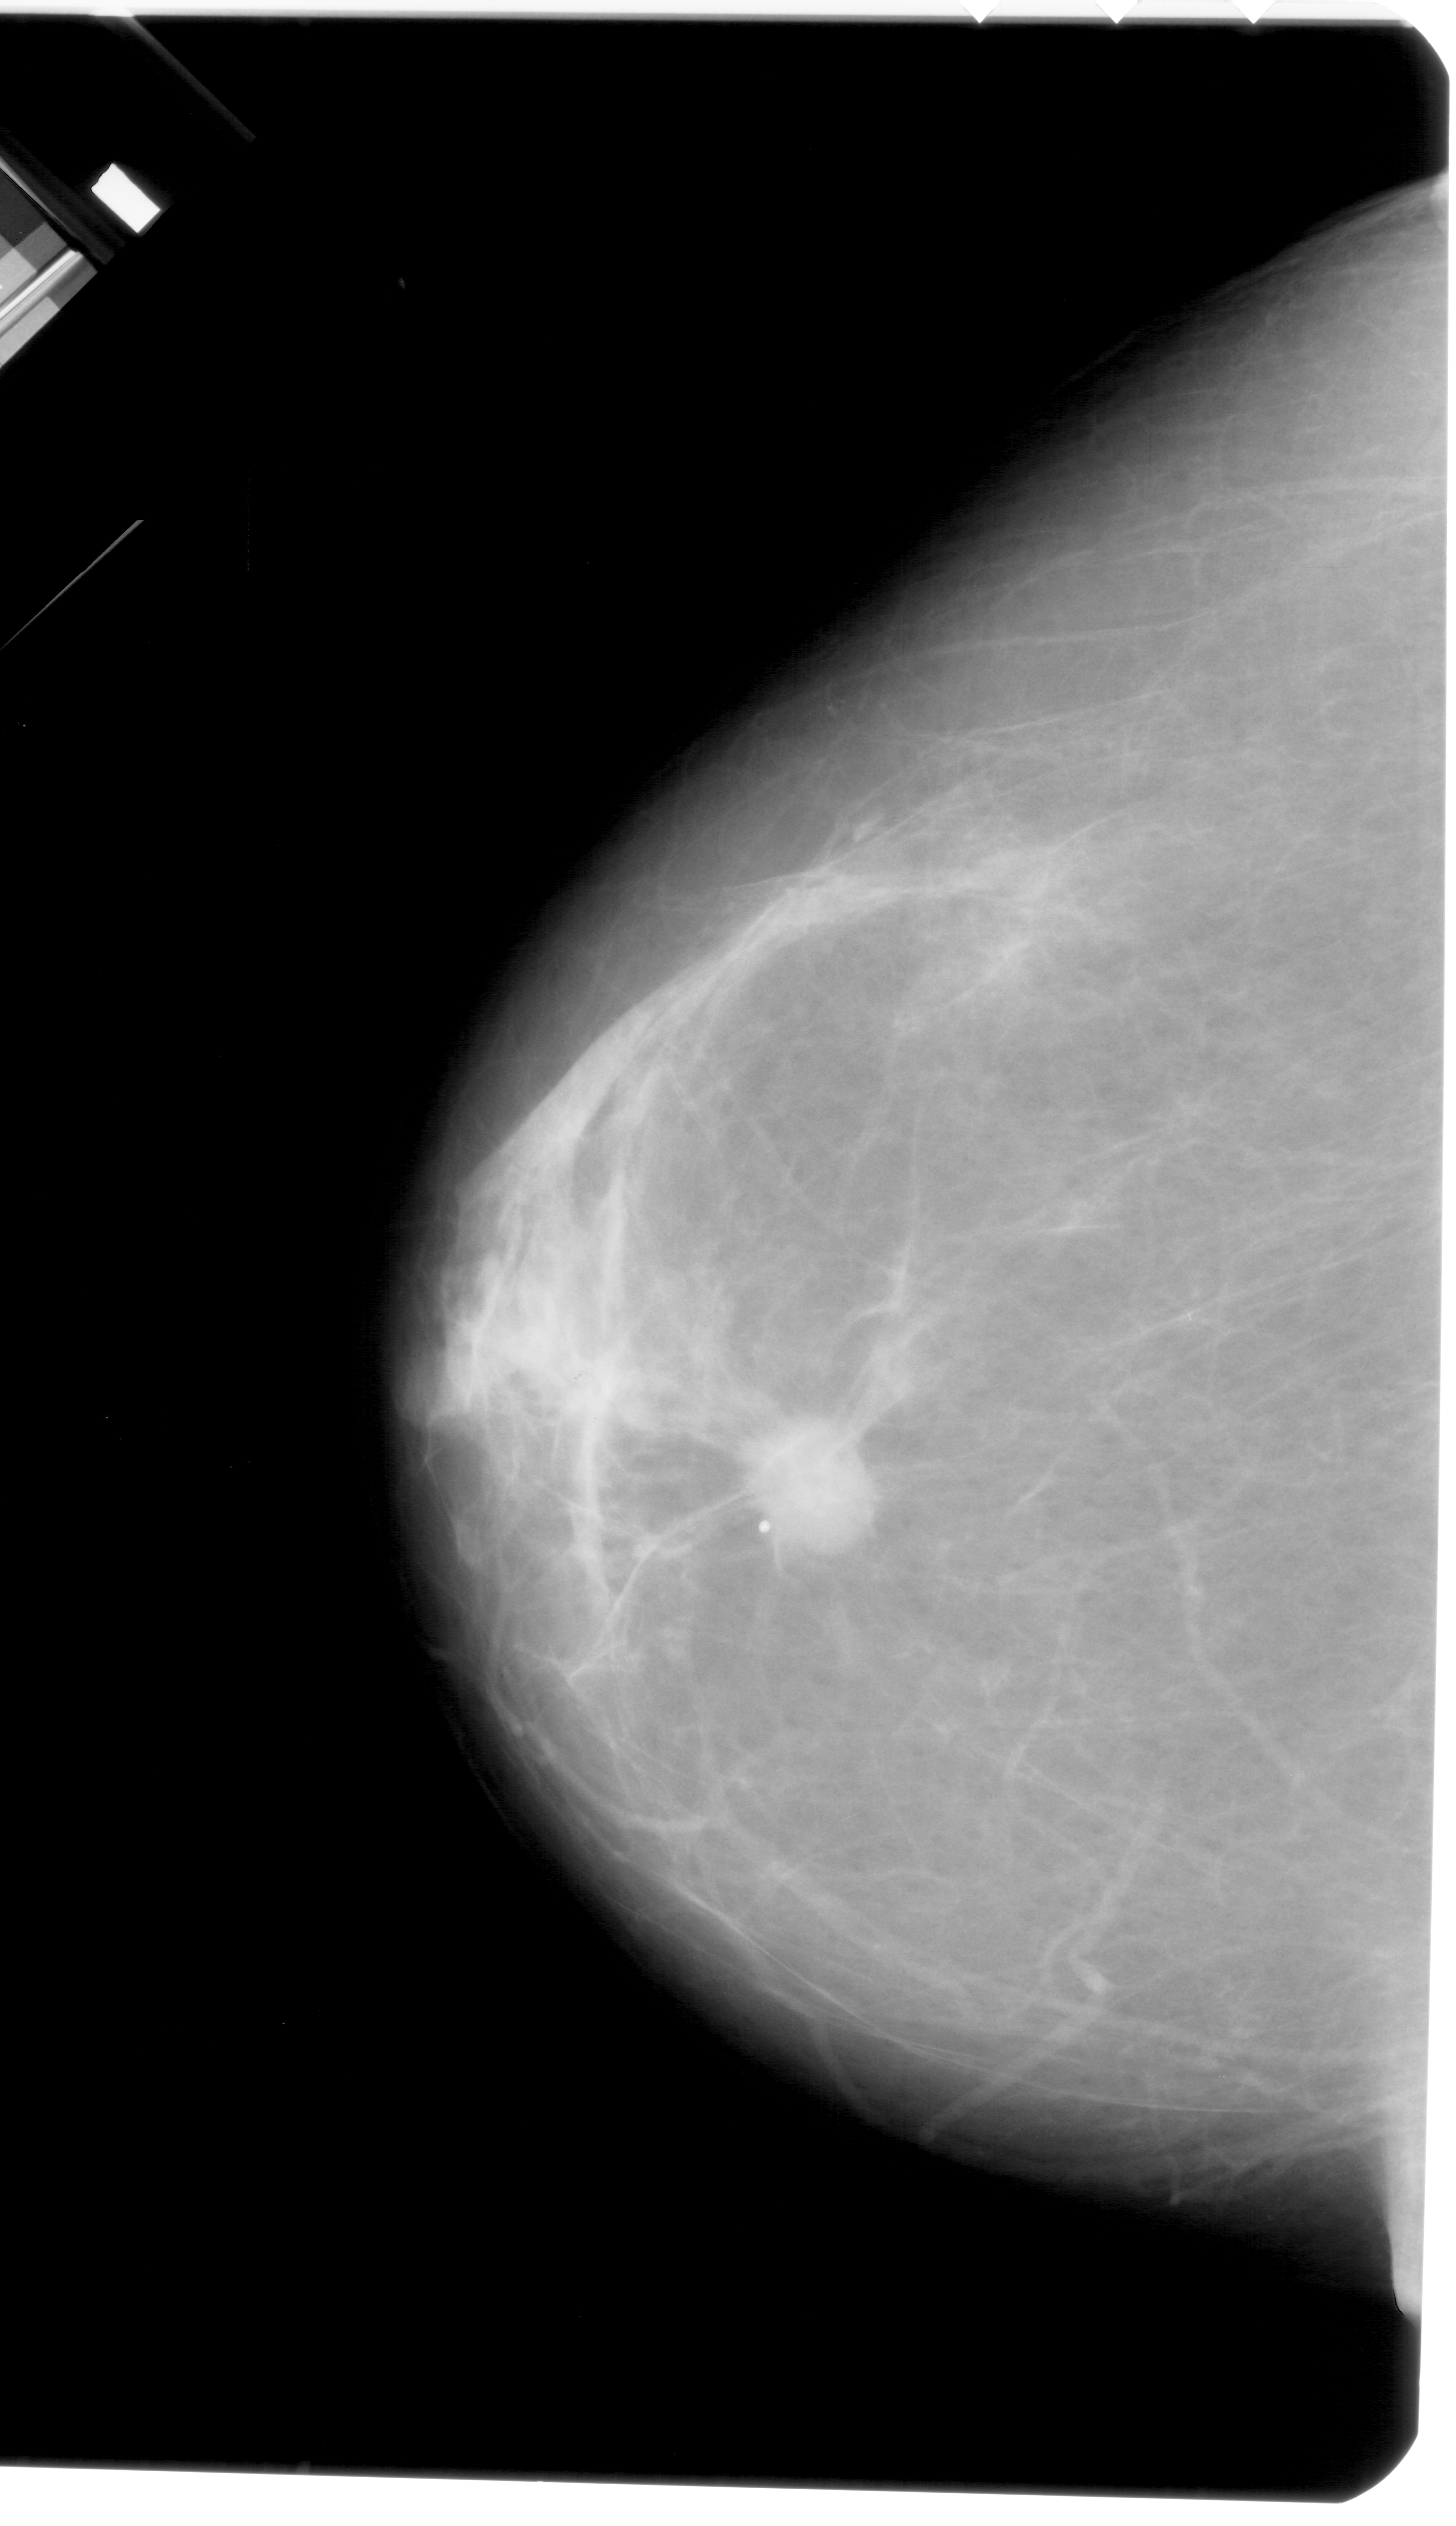
Scanned film-screen mammogram; left breast; craniocaudal (CC) view; breast composition: almost entirely fatty (BI-RADS density category 1 of 4).
Marked findings (only marked abnormalities are described; nothing is implied about the rest of the image): mass, shape oval, margins spiculated; BI-RADS assessment category 5; subtlety rating 5 on a 1 (subtle) to 5 (obvious) scale; pathology result (as recorded, not read from the image): malignant.